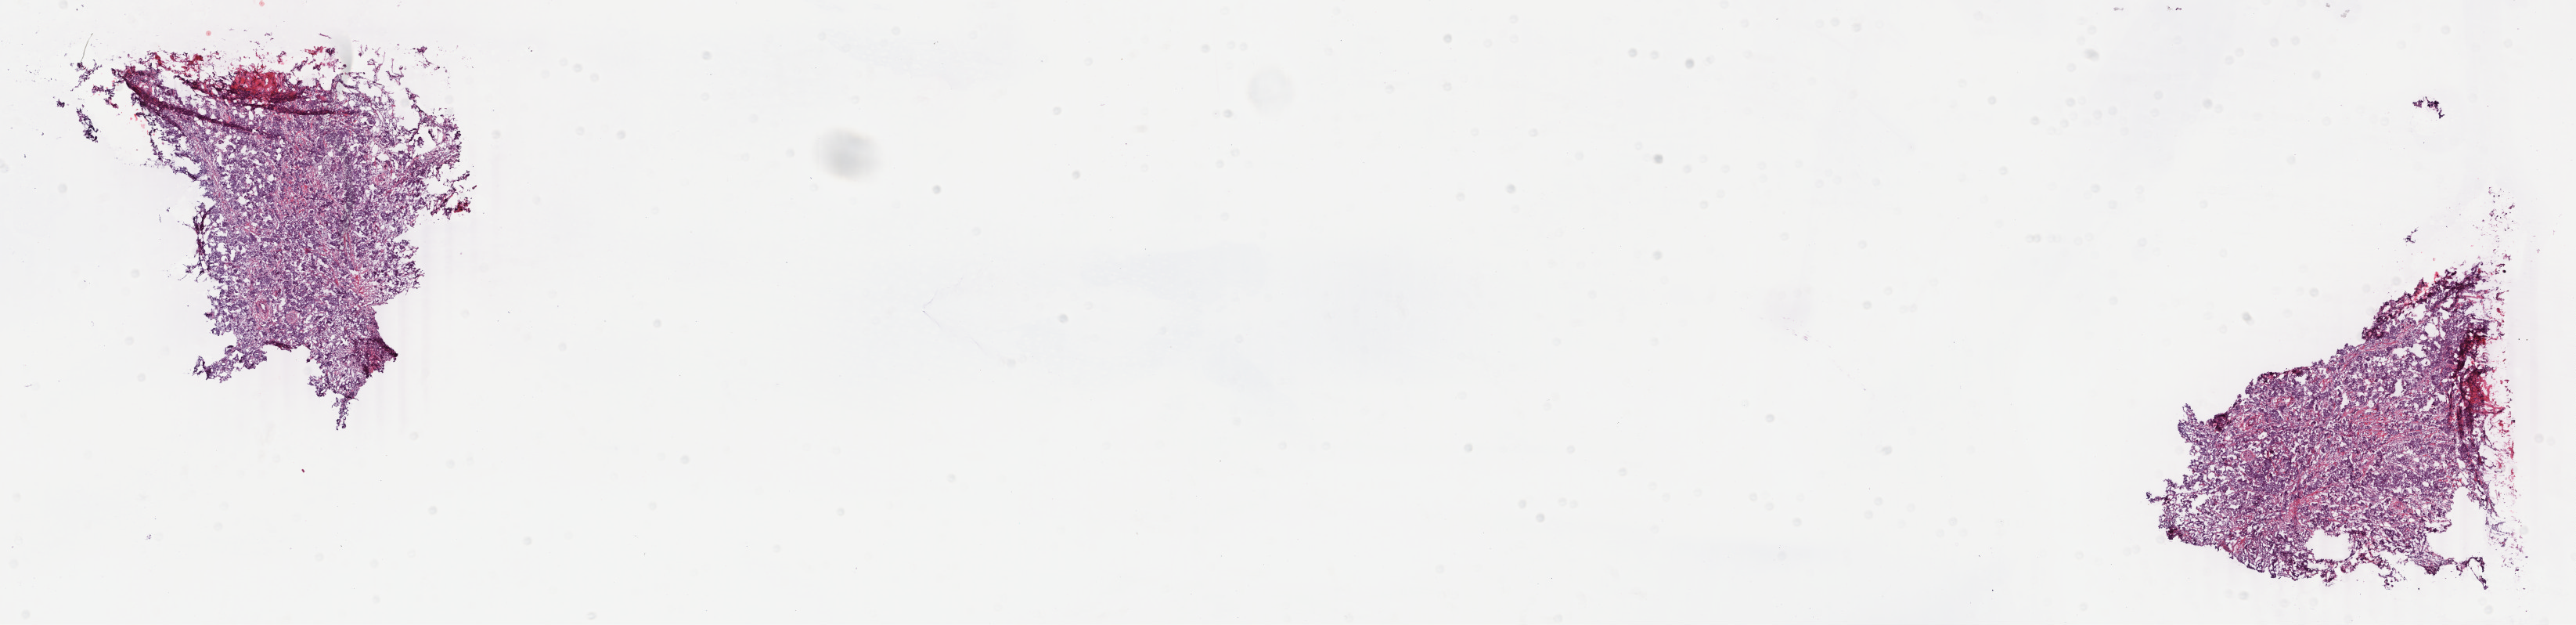
Digitized H&E-stained tissue section (whole slide), a low-resolution overview of the entire scanned area, about 26.2 x 6.3 mm; frozen section from the bottom of the tissue portion; sample: primary tumour, breast. Female patient; age at initial diagnosis 68 years. Slide review estimates, as recorded: tumour cells 89%, tumour nuclei 80%, normal cells 0%, stromal cells 10%, necrosis 1%. Infiltration values recorded for this section: lymphocyte infiltration 6%, monocyte infiltration 2%, neutrophil infiltration 0%.
AJCC pathologic stage: IIA. Histologic diagnosis: Infiltrating duct carcinoma, NOS. Lymph nodes positive (case pathology): 0 of 19 examined.